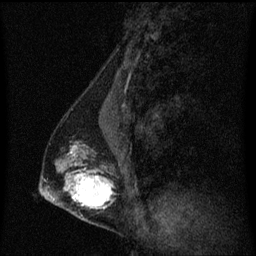
Breast MRI (dynamic contrast-enhanced), one sagittal slice. Slice 27 of 60 in the series (ordered by position). Dynamic contrast-enhanced series, image 2 of 3 at this slice position (ordered by acquisition). 1.5 T. TE 4.2 ms, TR 8.4 ms. 2 mm slice thickness. 256 × 256 image matrix. Patient: female, 40 years. Case-level facts recorded for this patient, not image findings: setting: breast cancer imaged before/during neoadjuvant chemotherapy; receptor status: triple-negative.
Outlined on this slice (semi-automatically segmented with operator editing):
- analysis volume of interest (the breast-tissue region the enhancement analysis was run in; not a lesion): bounding box <44,128,120,221> (left, top, right, bottom; pixels)
- tumour enhancement mask (voxels above the 70 % enhancement threshold inside the analysis volume of interest): <66,146,113,209>